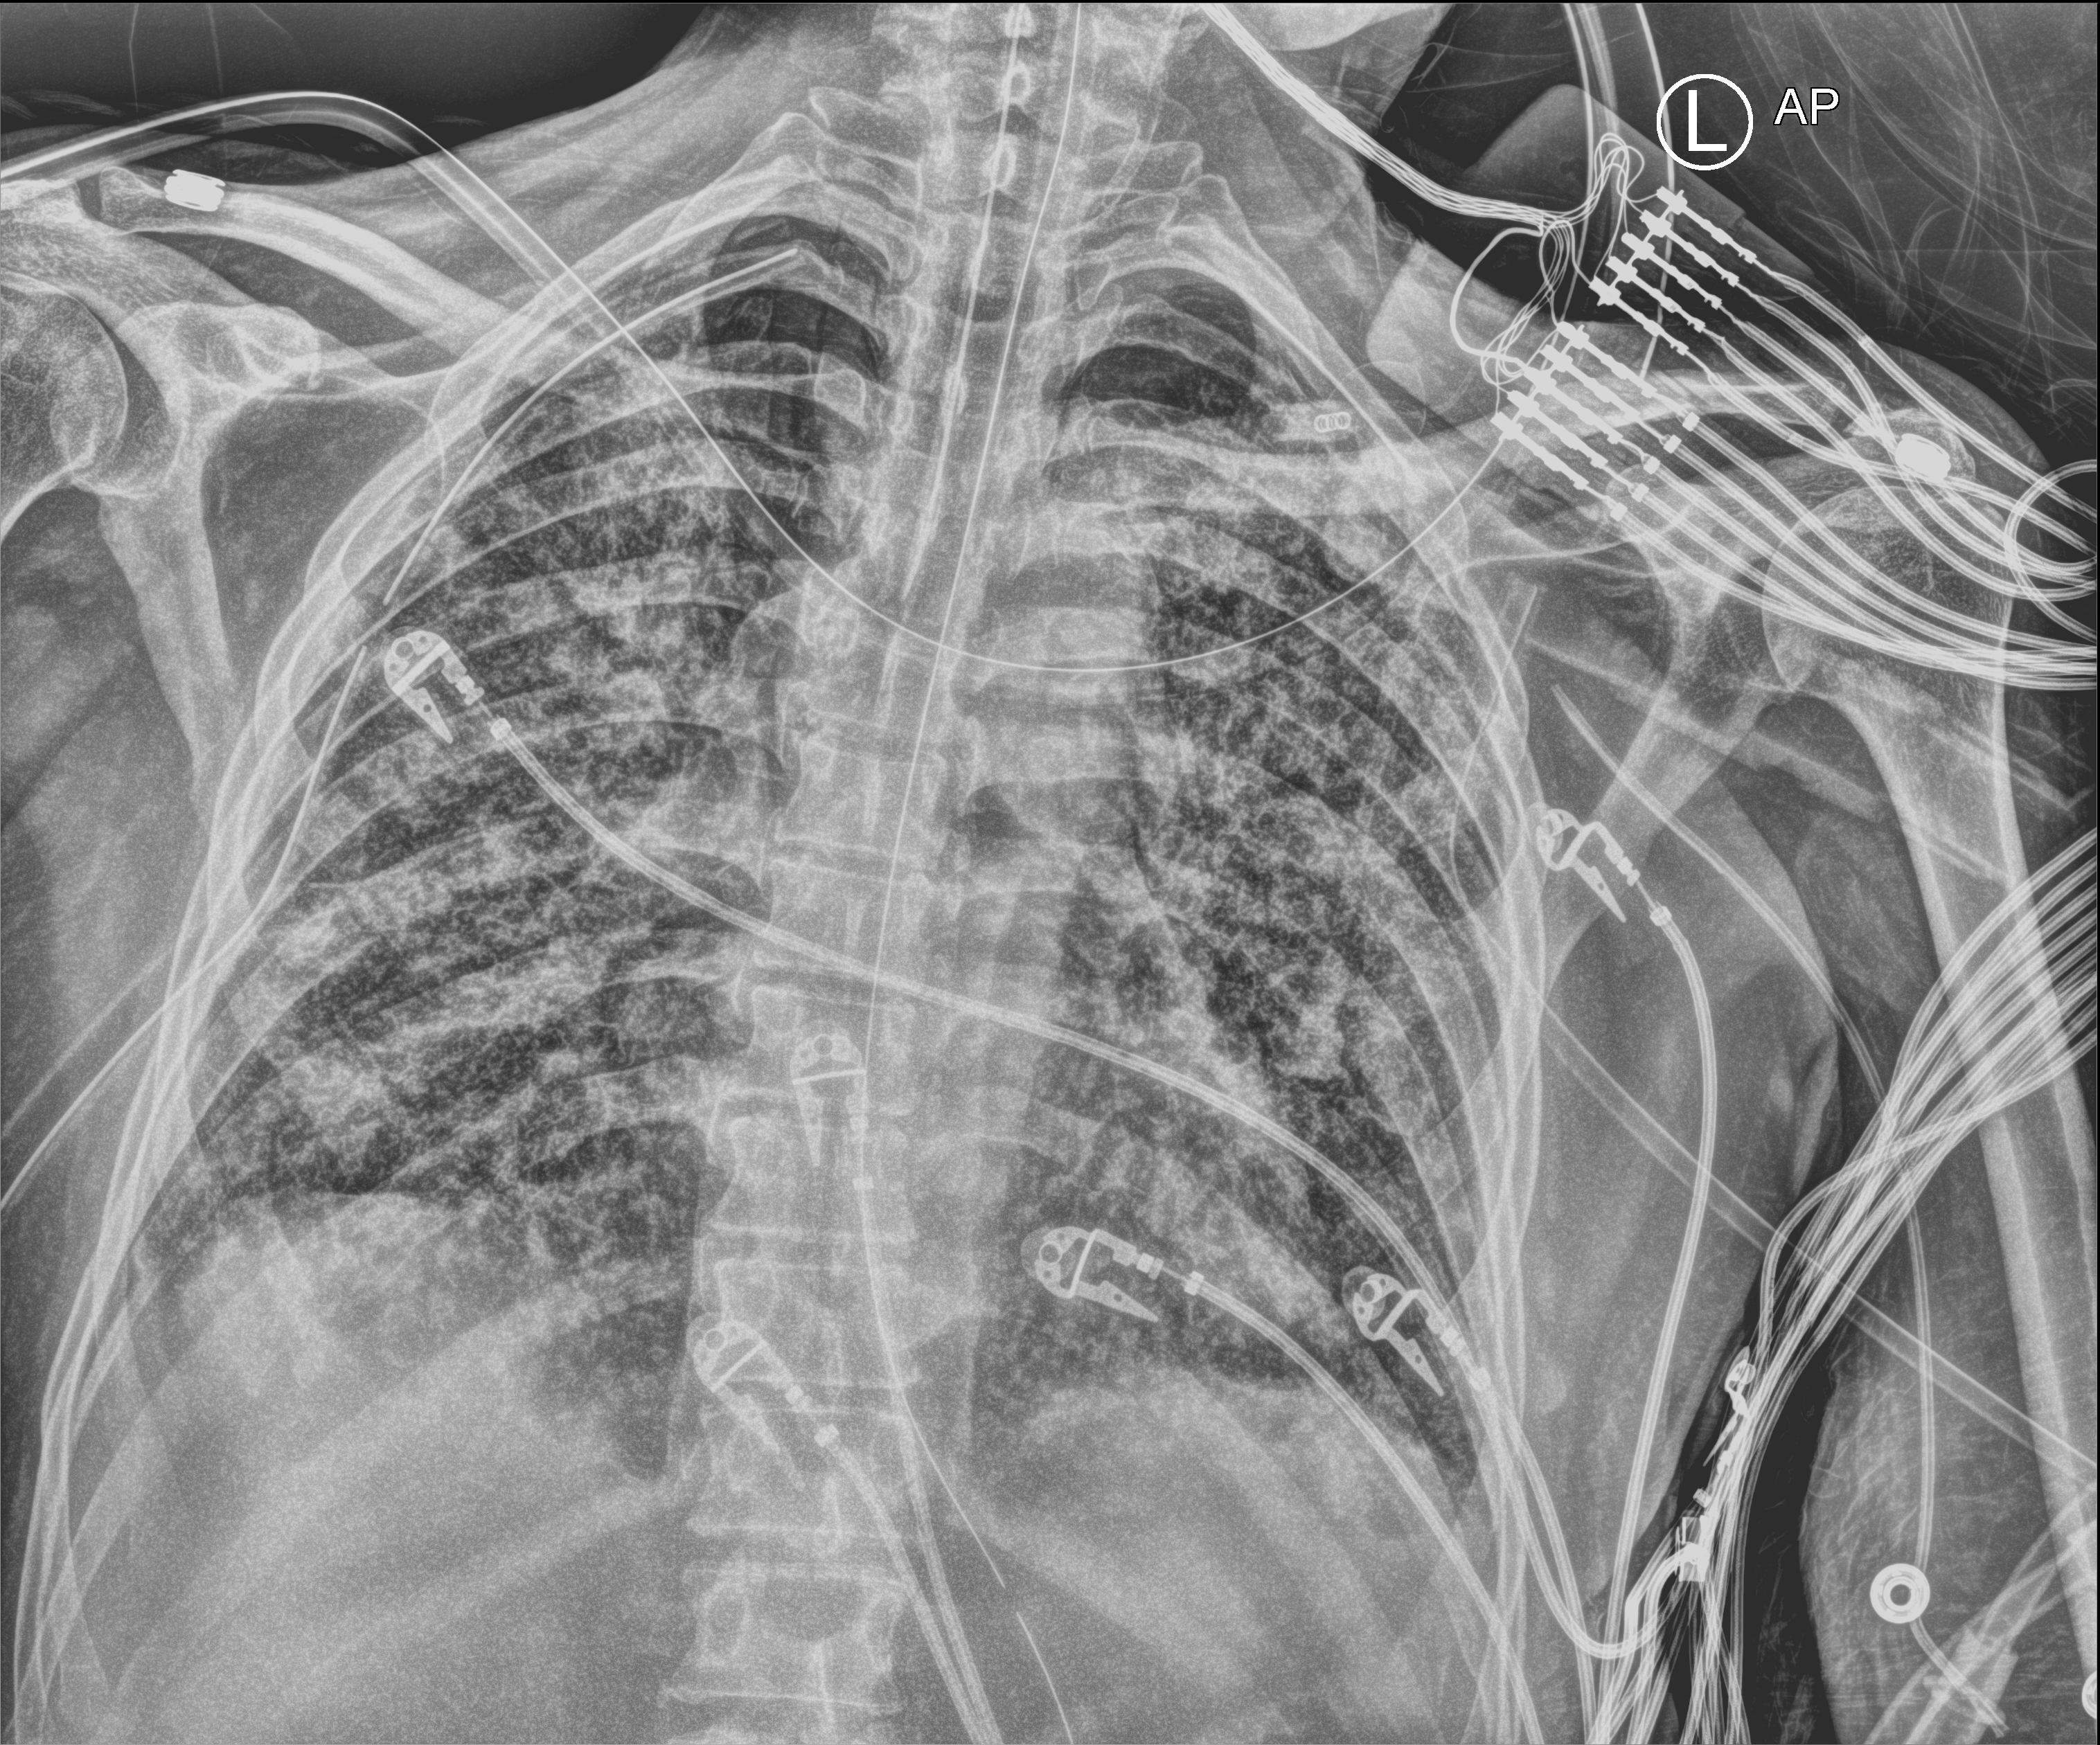
Chest X-ray (portable); anteroposterior (AP) projection. Male patient hospitalised with COVID-19, age 60–74 years.
Admission-level facts for this patient (not findings on this image; timing relative to this image not recorded): admitted to intensive care during this hospital stay: yes; length of hospital stay: 65 days.